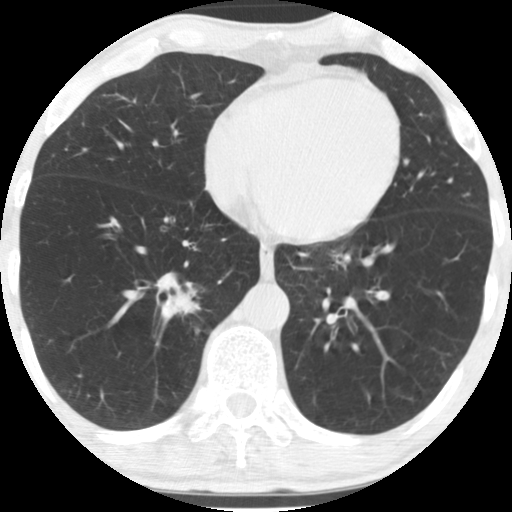
Chest CT (low-dose screening protocol), one axial image. First (baseline) screen. Lung window (W 1500 / L -600 HU). 2.5 mm slice thickness. Standard (soft-tissue) reconstruction kernel (STANDARD). 120 kVp. Slice 116 of 170 in the series. 512 × 512 image matrix, field of view 290 × 290 mm. Male, age 67 years at enrolment. Former smoker at enrolment.
Lesion marked by an expert reader, bounding box (x1, y1, x2, y2) in pixels: (156, 275, 219, 330). Screening reader's record for this exam (one nodule recorded; not confirmed to be the boxed lesion): non-calcified nodule or mass ≥4 mm, right lower lobe, 16 × 16 mm, spiculated (stellate) margins, soft tissue attenuation. Official screen result: positive, change unspecified: nodule(s) >= 4 mm or enlarging nodule(s), mass(es), or other non-specific abnormalities suspicious for lung cancer. Lung cancer was diagnosed 49 days after this screen: squamous cell carcinoma, NOS, right lower lobe, moderately differentiated (G2), stage IA (AJCC 6th edition), 20 mm at pathology.